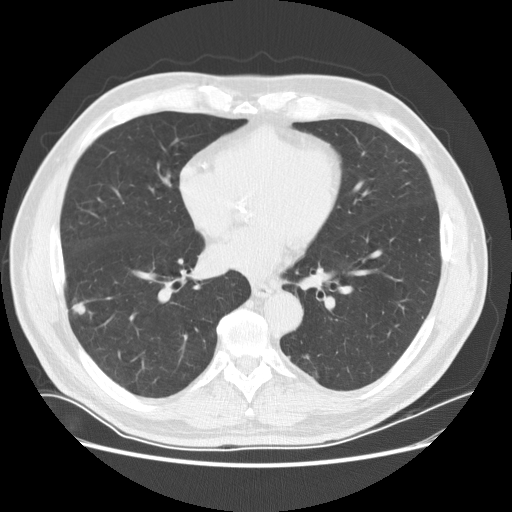
Low-dose screening chest CT, one axial slice. Slice 77 of 169 in the series (ordered by position). Reconstruction kernel STANDARD. 120 kVp. Lung window (W 1500 / L -600 HU). 2.5 mm slice thickness. 512 × 512 image matrix.
Structures marked on this image (outlined manually by an expert reader):
- lesion 1 (tumor, lower lobe of right lung): bounding box (x1, y1, x2, y2) in pixels: (72, 303, 86, 315)